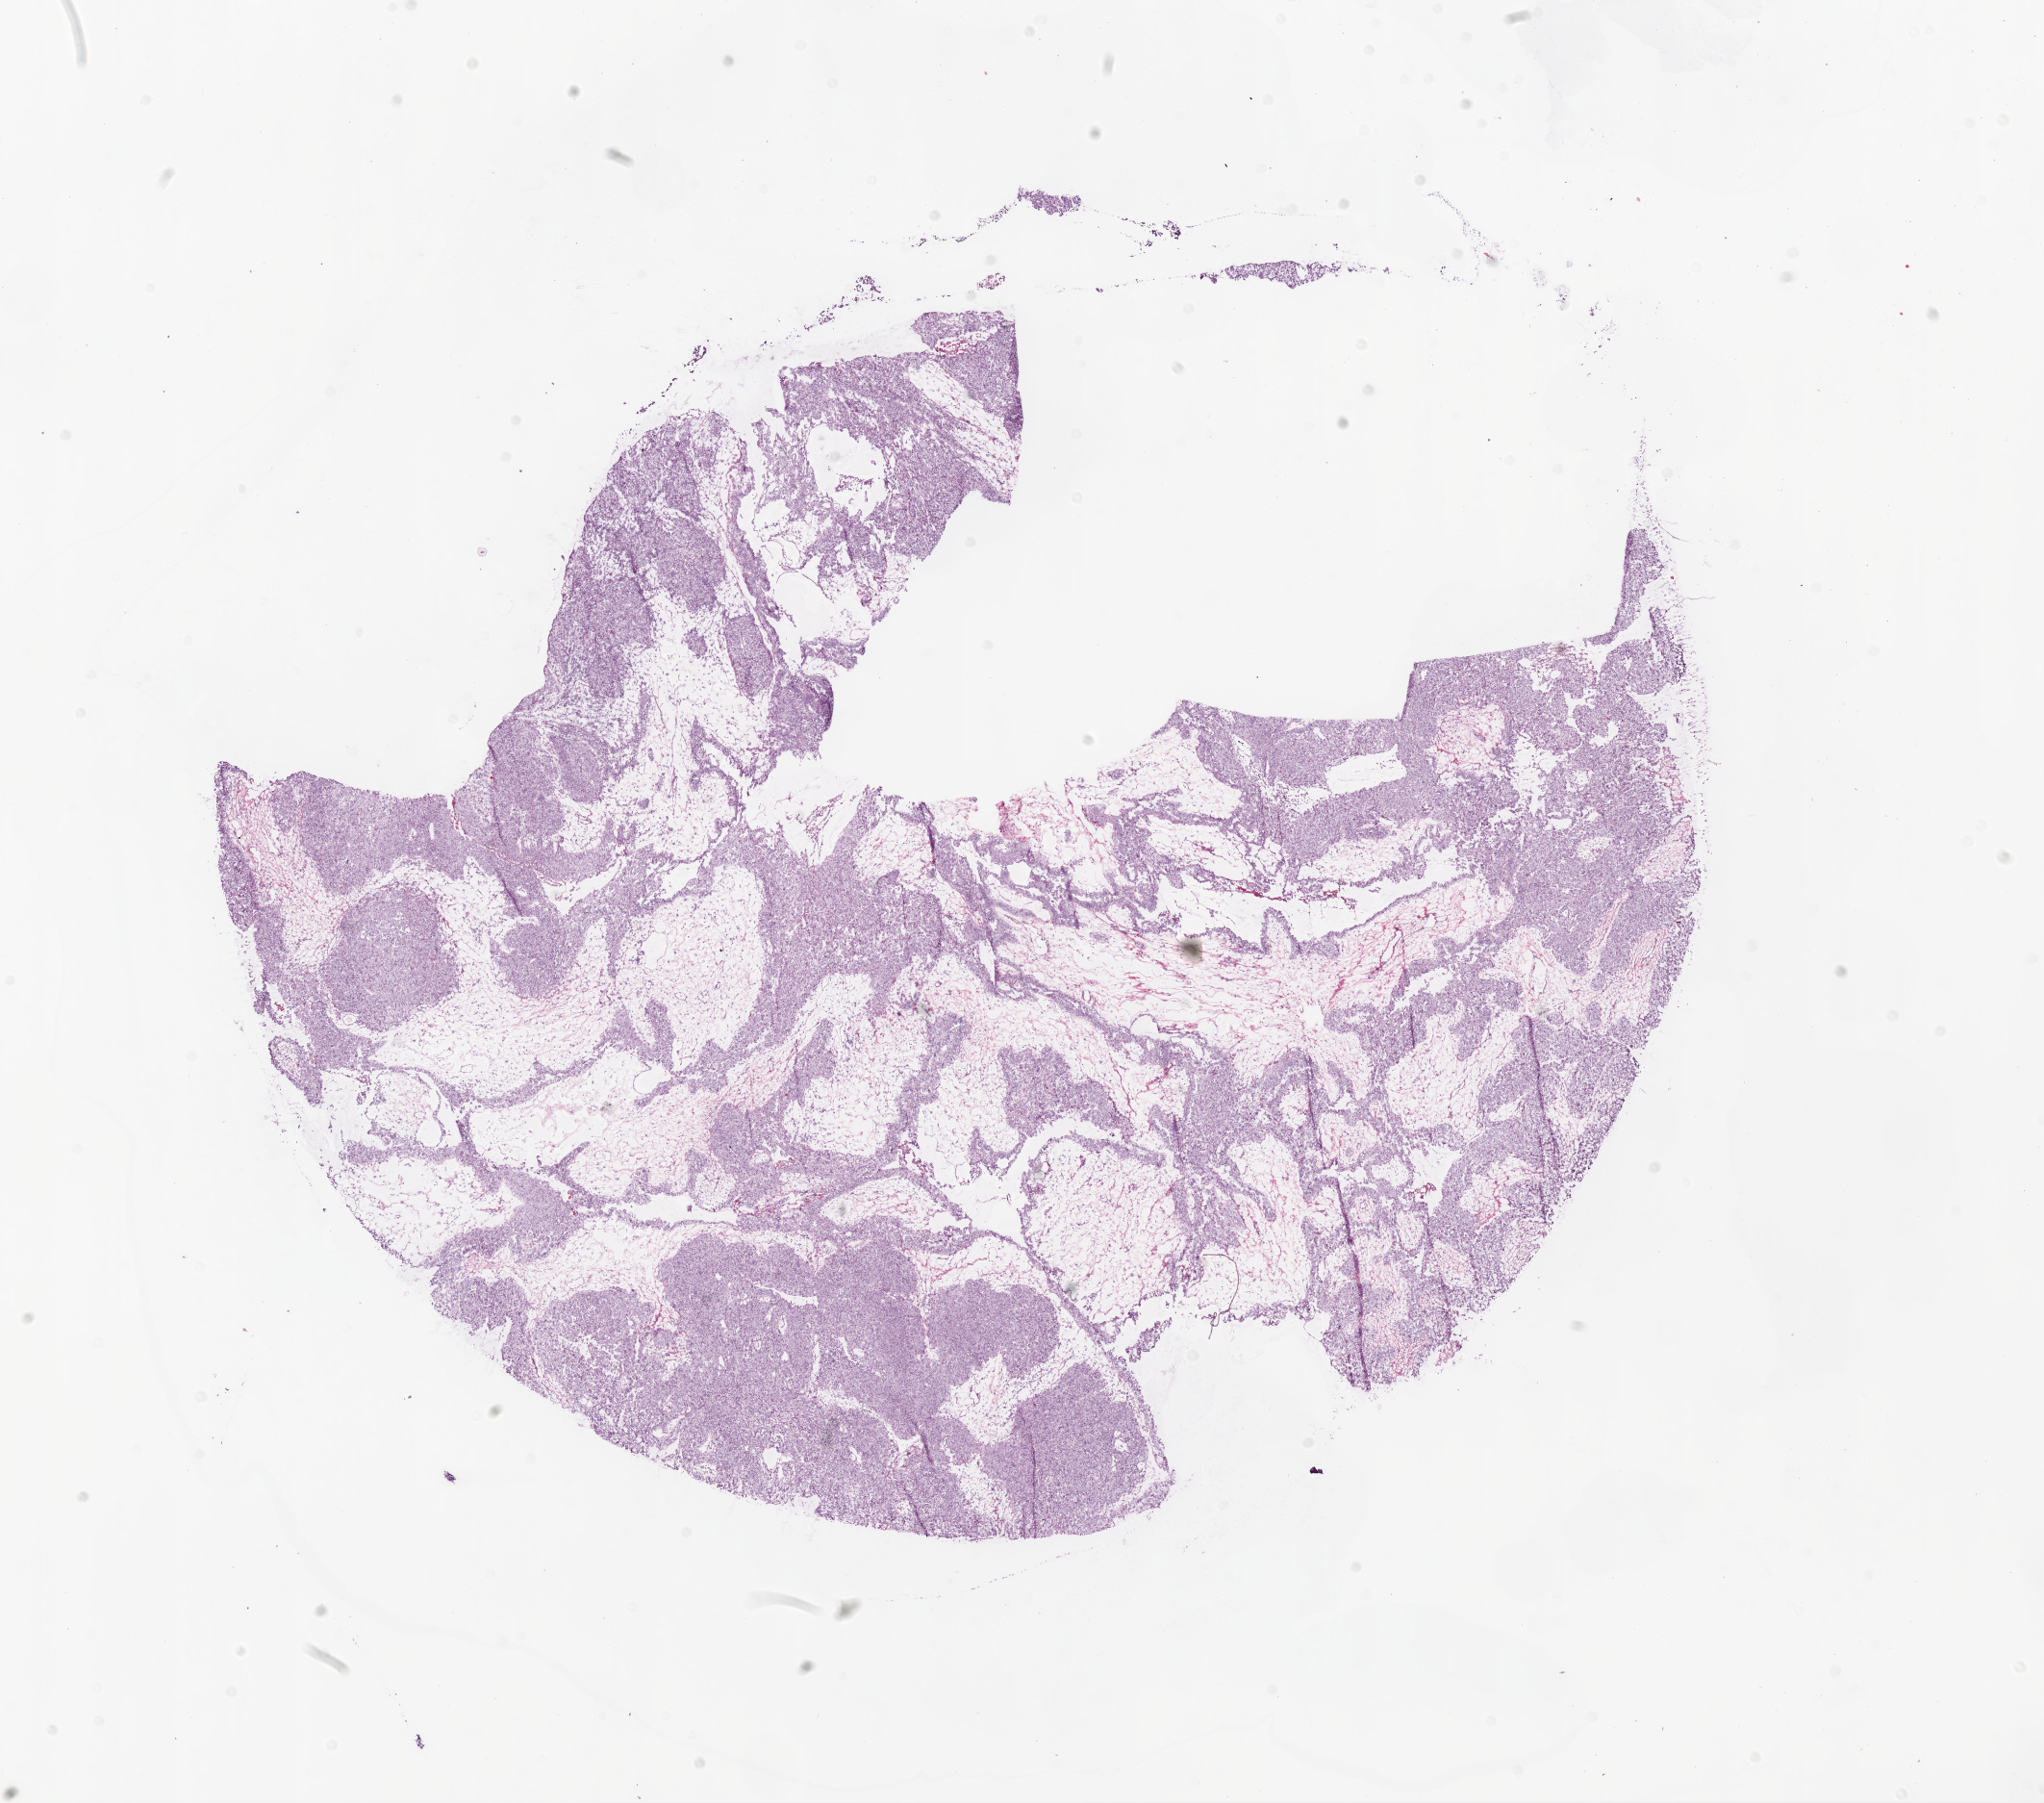
H&E-stained whole-slide image, a low-resolution overview of the entire scanned area, about 17.1 x 15.0 mm; frozen section from the bottom of the tissue portion; ovary, primary tumour sample. Female, age 77 years at initial diagnosis. Histologic grade: G3 (poorly differentiated). Pathologist review of this section (percent, as recorded): tumour cells 60%, tumour nuclei 85%, normal cells 0%, stromal cells 40%, necrosis 0%. Infiltration values recorded for this section: lymphocyte infiltration 10%.
FIGO stage: IIIC. Laterality: right. Histologic diagnosis: Serous cystadenocarcinoma, NOS.